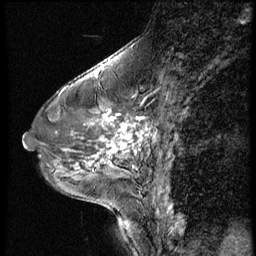
Breast MRI (dynamic contrast-enhanced), one sagittal slice; dynamic contrast-enhanced series, image 2 of 3 at this slice position (ordered by acquisition); 1.5 T; TE 4.2 ms, TR 9 ms; 2.5 mm slice thickness; 256 × 256 image matrix, field of view 180 × 180 mm. Female patient, age 46 years. Case-level facts recorded for this patient, not image findings: setting: breast cancer imaged before/during neoadjuvant chemotherapy; receptor status: HER2-positive.
Outlined on this slice (semi-automatic segmentation, software-assisted and operator-edited):
- analysis volume of interest (the breast-tissue region the enhancement analysis was run in; not a lesion): bounding box [x1, y1, x2, y2] px = [64, 98, 174, 182]
- tumour enhancement mask (voxels above the 140 % enhancement threshold inside the analysis volume of interest): [79, 113, 149, 168]